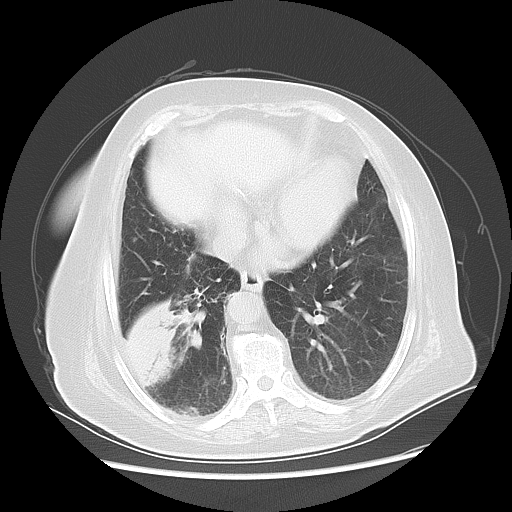
Chest CT, one axial slice; slice 20 of 56 in the series (ordered by position); reconstruction kernel LUNG; 120 kVp; lung window (W 1500 / L -600 HU); 512 × 512 image matrix. Female patient, age 73 years. From the clinical record (not read from this slice): clinical TNM (as recorded): T3 N0 M0.
Annotated regions visible in this slice (bounding box drawn by a radiologist):
- lung tumour (recorded histology: adenocarcinoma): box from (x=121, y=298) to (x=196, y=389) px